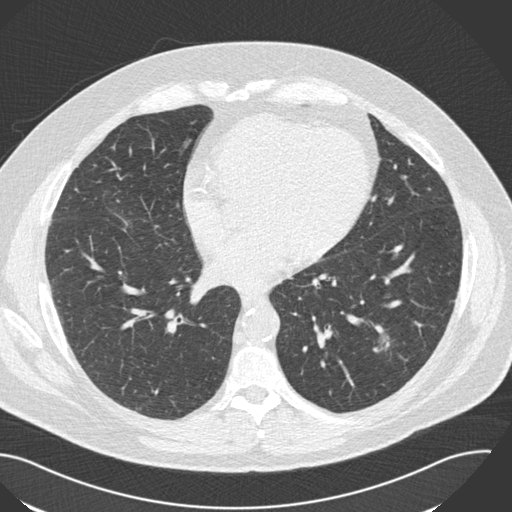
Low-dose screening chest CT, one axial slice. Position 75 of 153 along the scan axis. Reconstruction kernel B30f. 120 kVp. Lung window (W 1500 / L -600 HU). 512 × 512 image matrix, field of view 394 × 394 mm.
Annotated regions visible in this slice (outlined manually by an expert reader):
- lesion 1 (tumor, lower lobe of left lung): bounding box <373,332,389,352> (left, top, right, bottom; pixels)